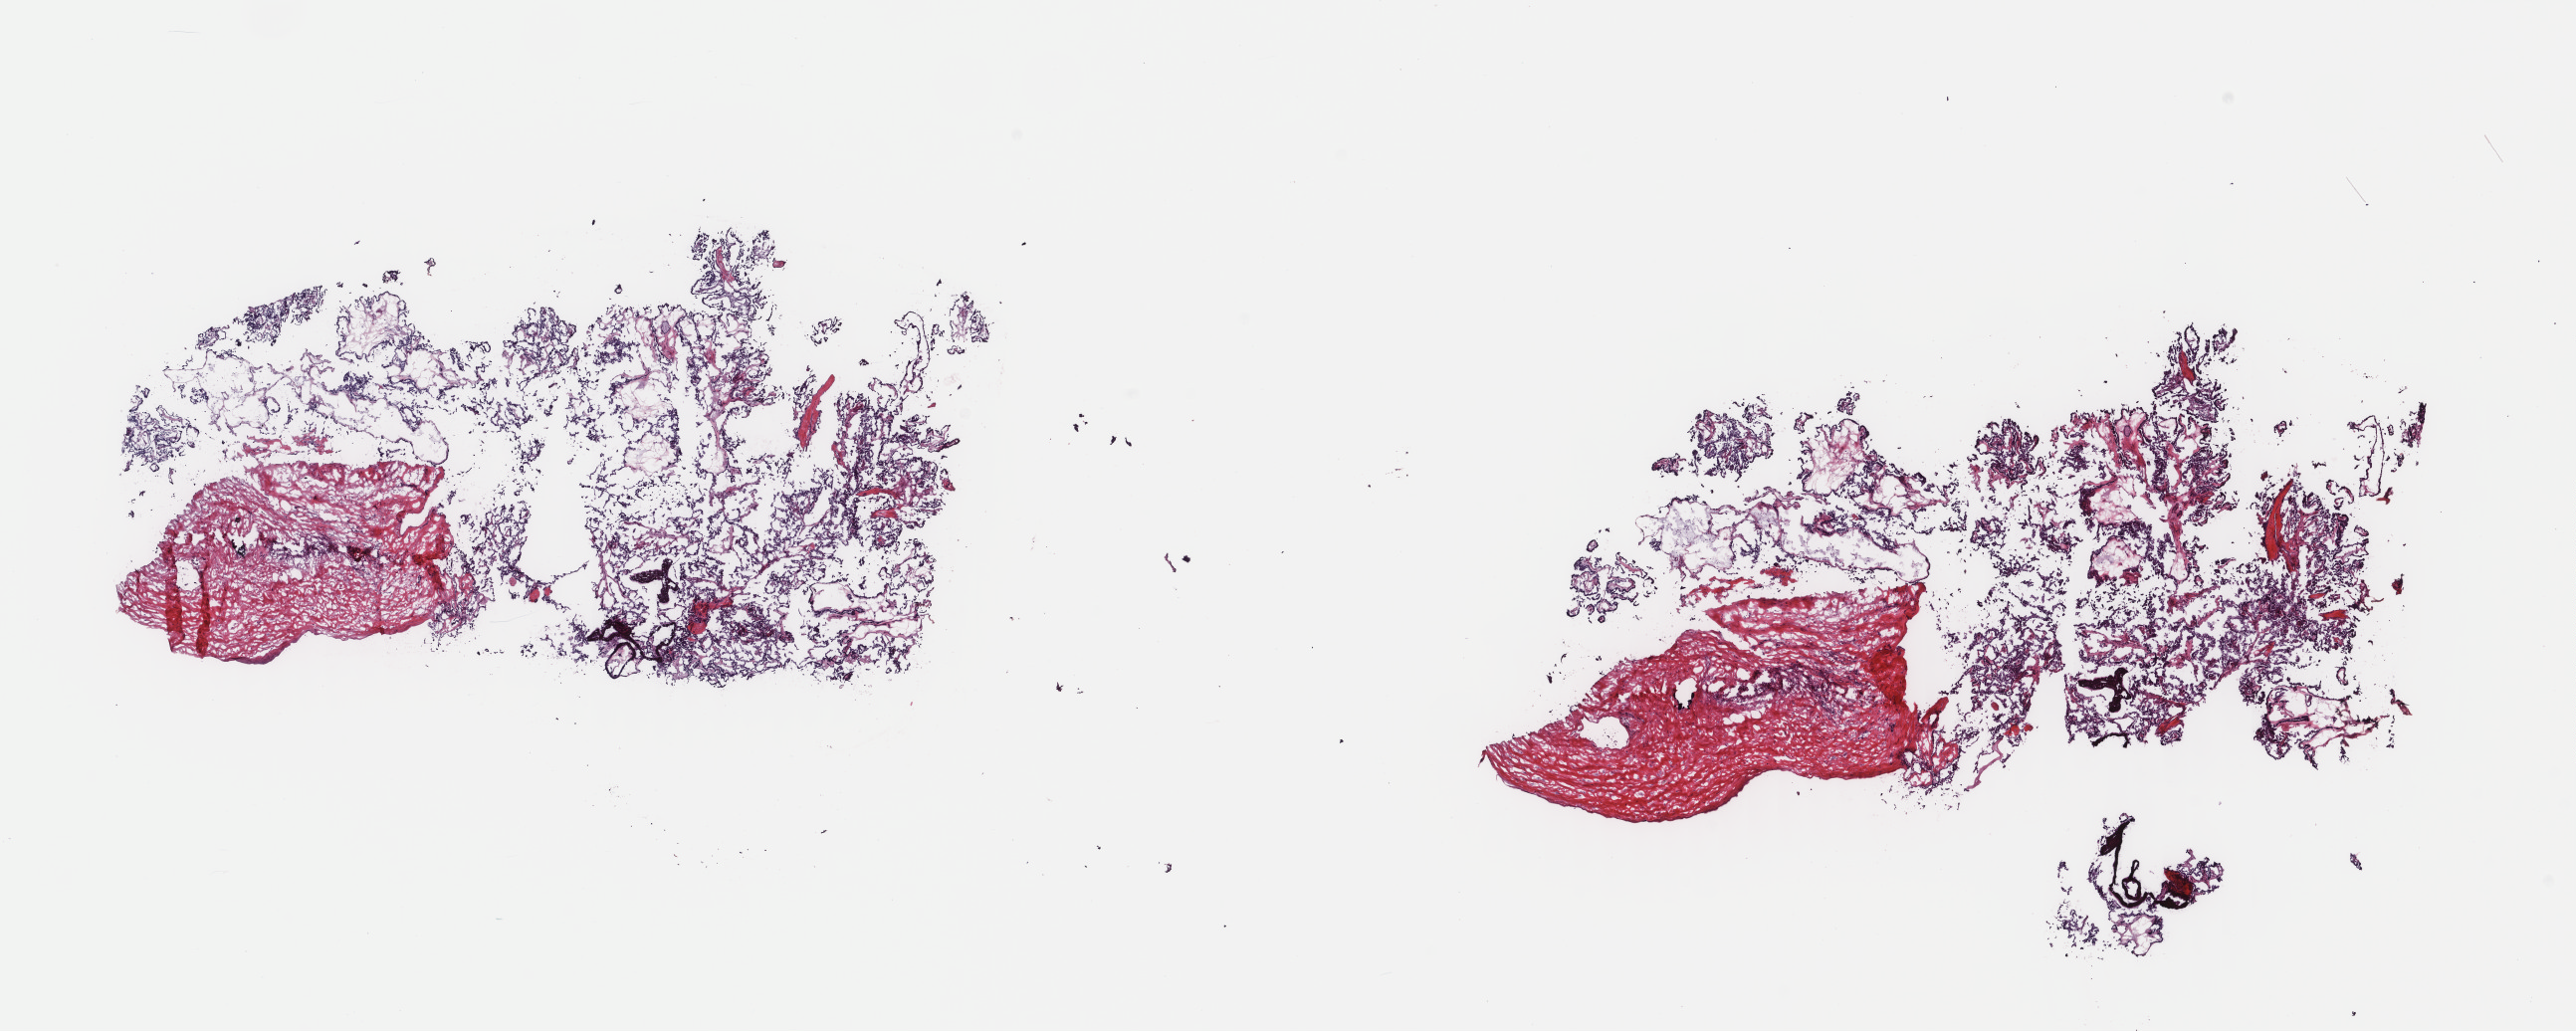
H&E-stained whole-slide image, shown as a low-resolution overview of the whole scanned area (about 20.5 x 8.2 mm, from a 40x scan). Frozen section from the top of the tissue portion. Thyroid, primary tumour sample. Male, age 39 years at initial diagnosis. Pathologist review of this section (percent, as recorded): tumour cells 75%, tumour nuclei 90%, normal cells 0%, stromal cells 25%, necrosis 0%. Infiltration values recorded for this section: lymphocyte infiltration 1%, monocyte infiltration 1%, neutrophil infiltration 0%.
Diagnosis: Papillary adenocarcinoma, NOS (thyroid gland). AJCC pathologic stage: I. Lymph nodes positive (case pathology): 0 of 19 examined.